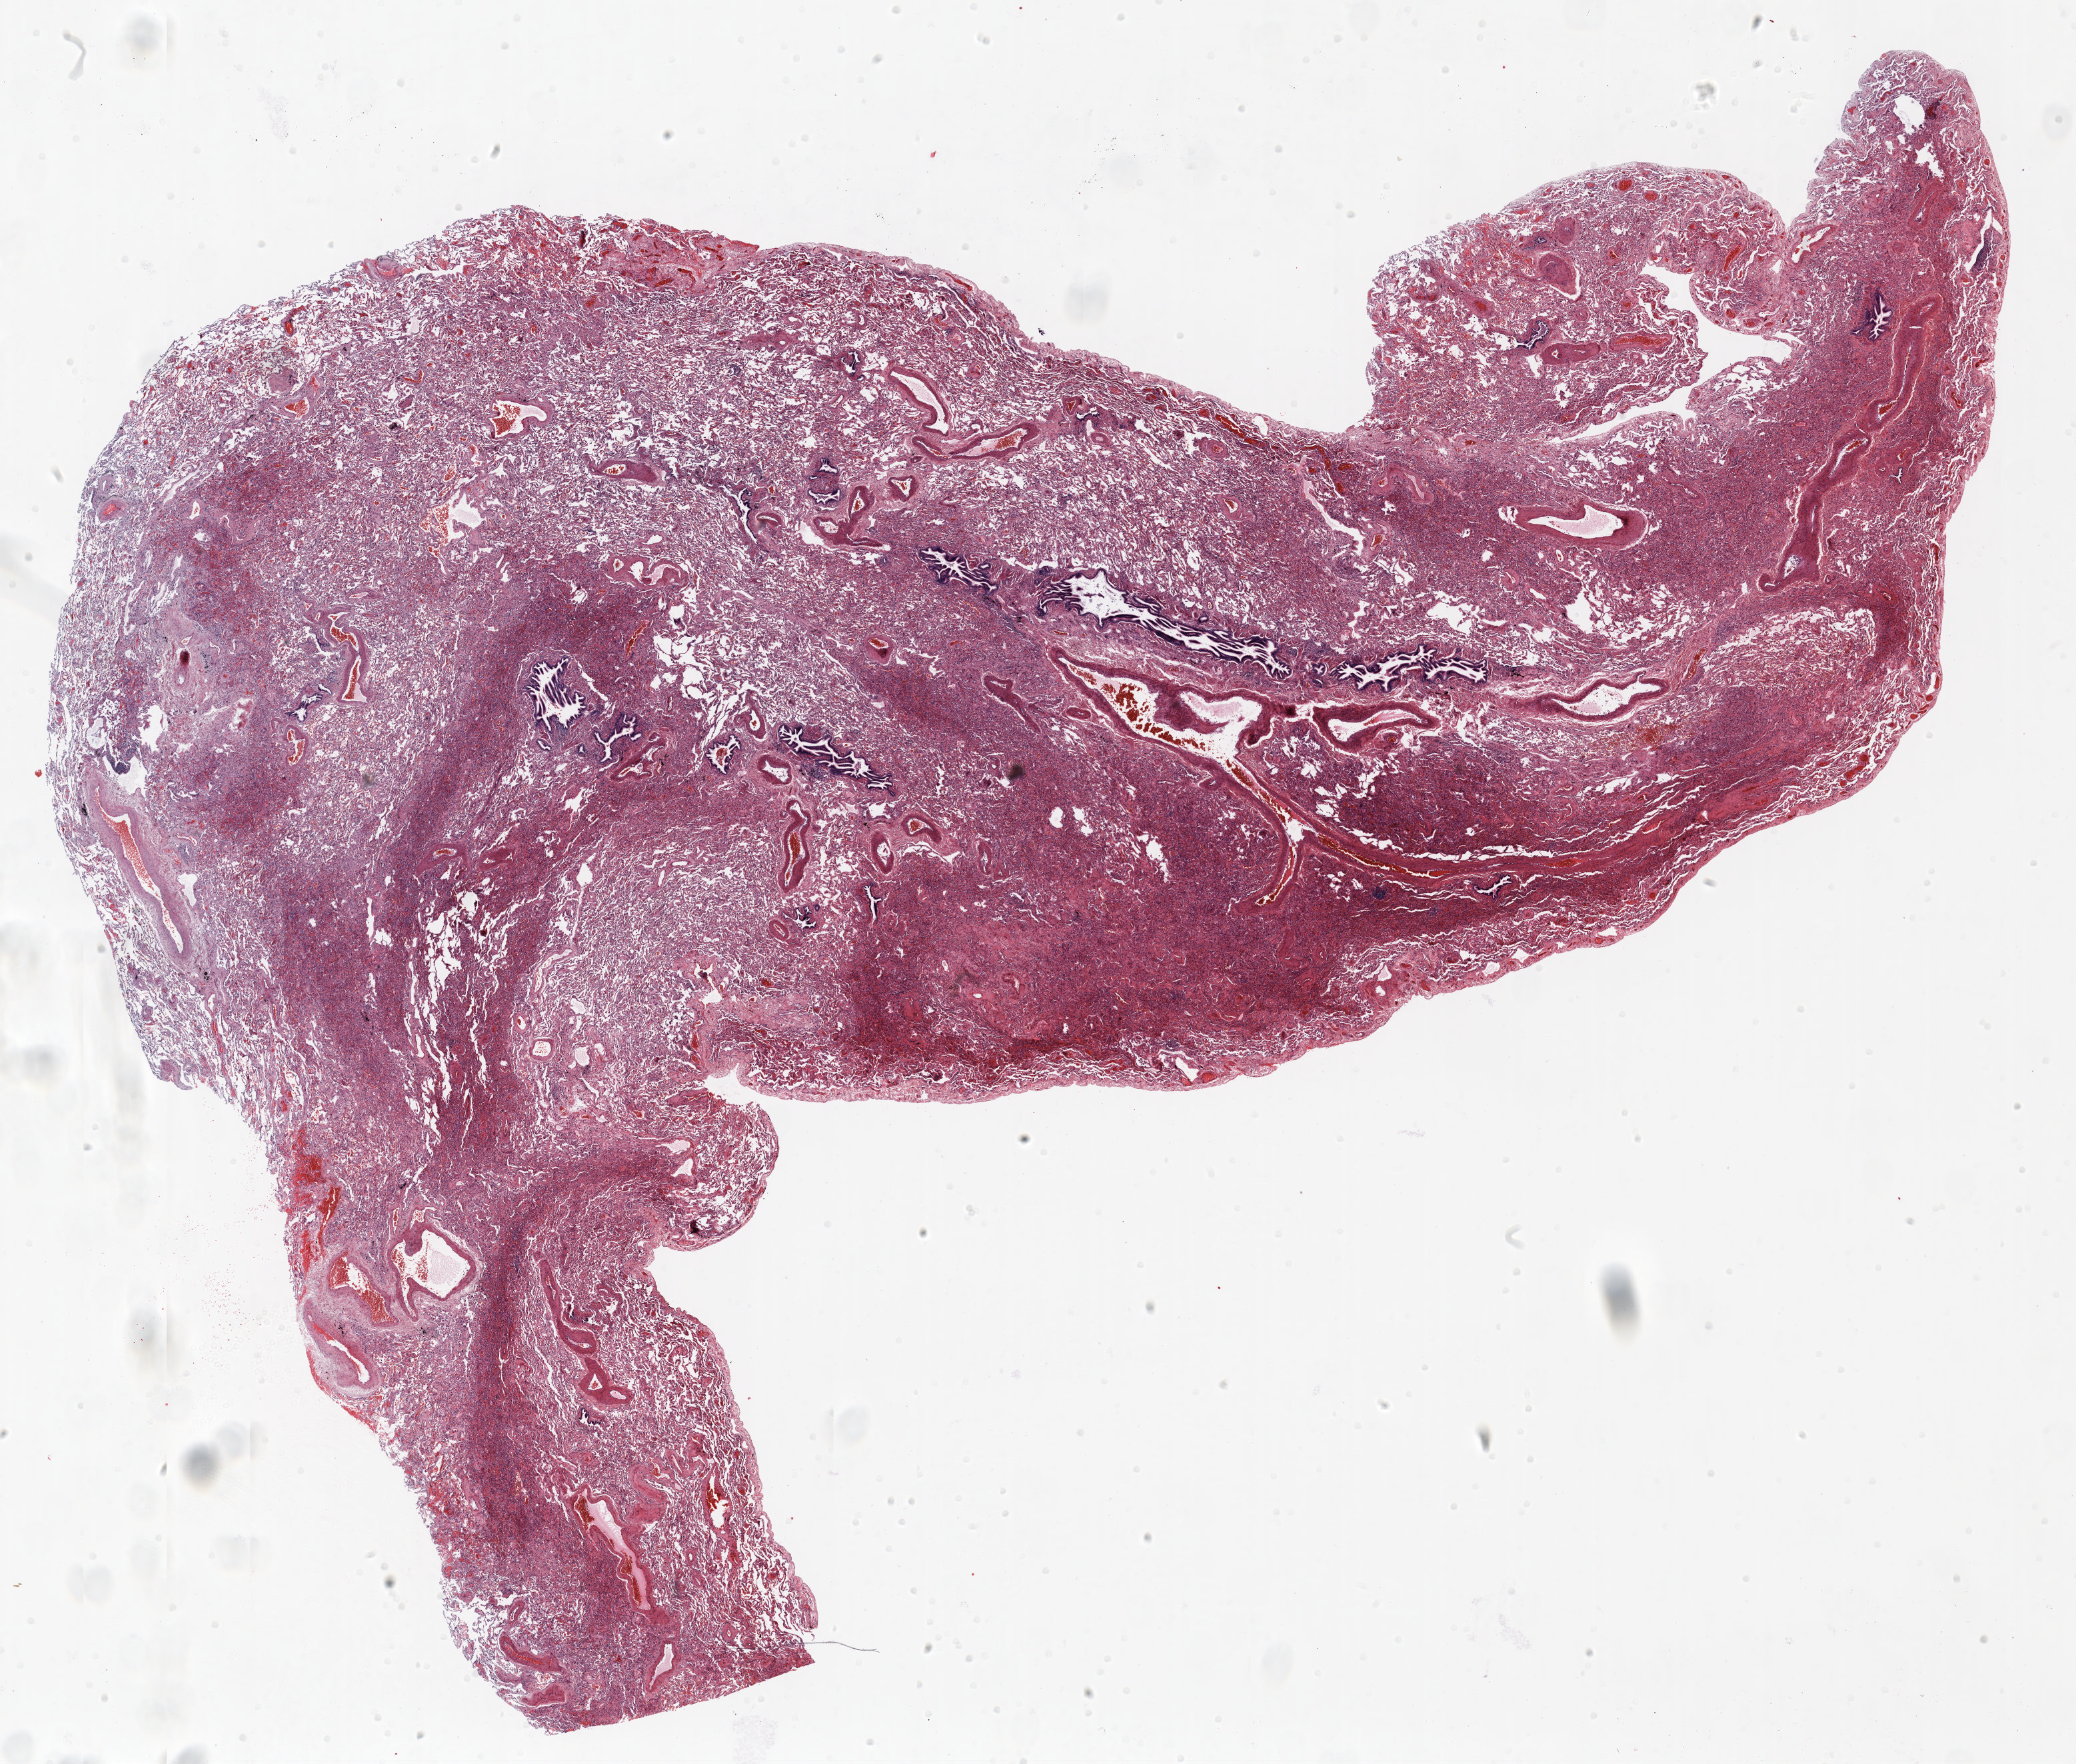
Whole-slide histology image, H&E-stained — whole scanned area (about 25.0 x 21.3 mm, from a 20x scan) shown as a low-resolution overview. FFPE section. Lung. Male, age 63 at enrolment. Grade: moderately differentiated (G2).
• primary tumour location (clinical record): left upper lobe
• stage (AJCC 6th edition): IA
• tumour size (pathology): 14 mm
• participant's lung-cancer diagnosis: Adenocarcinoma, NOS